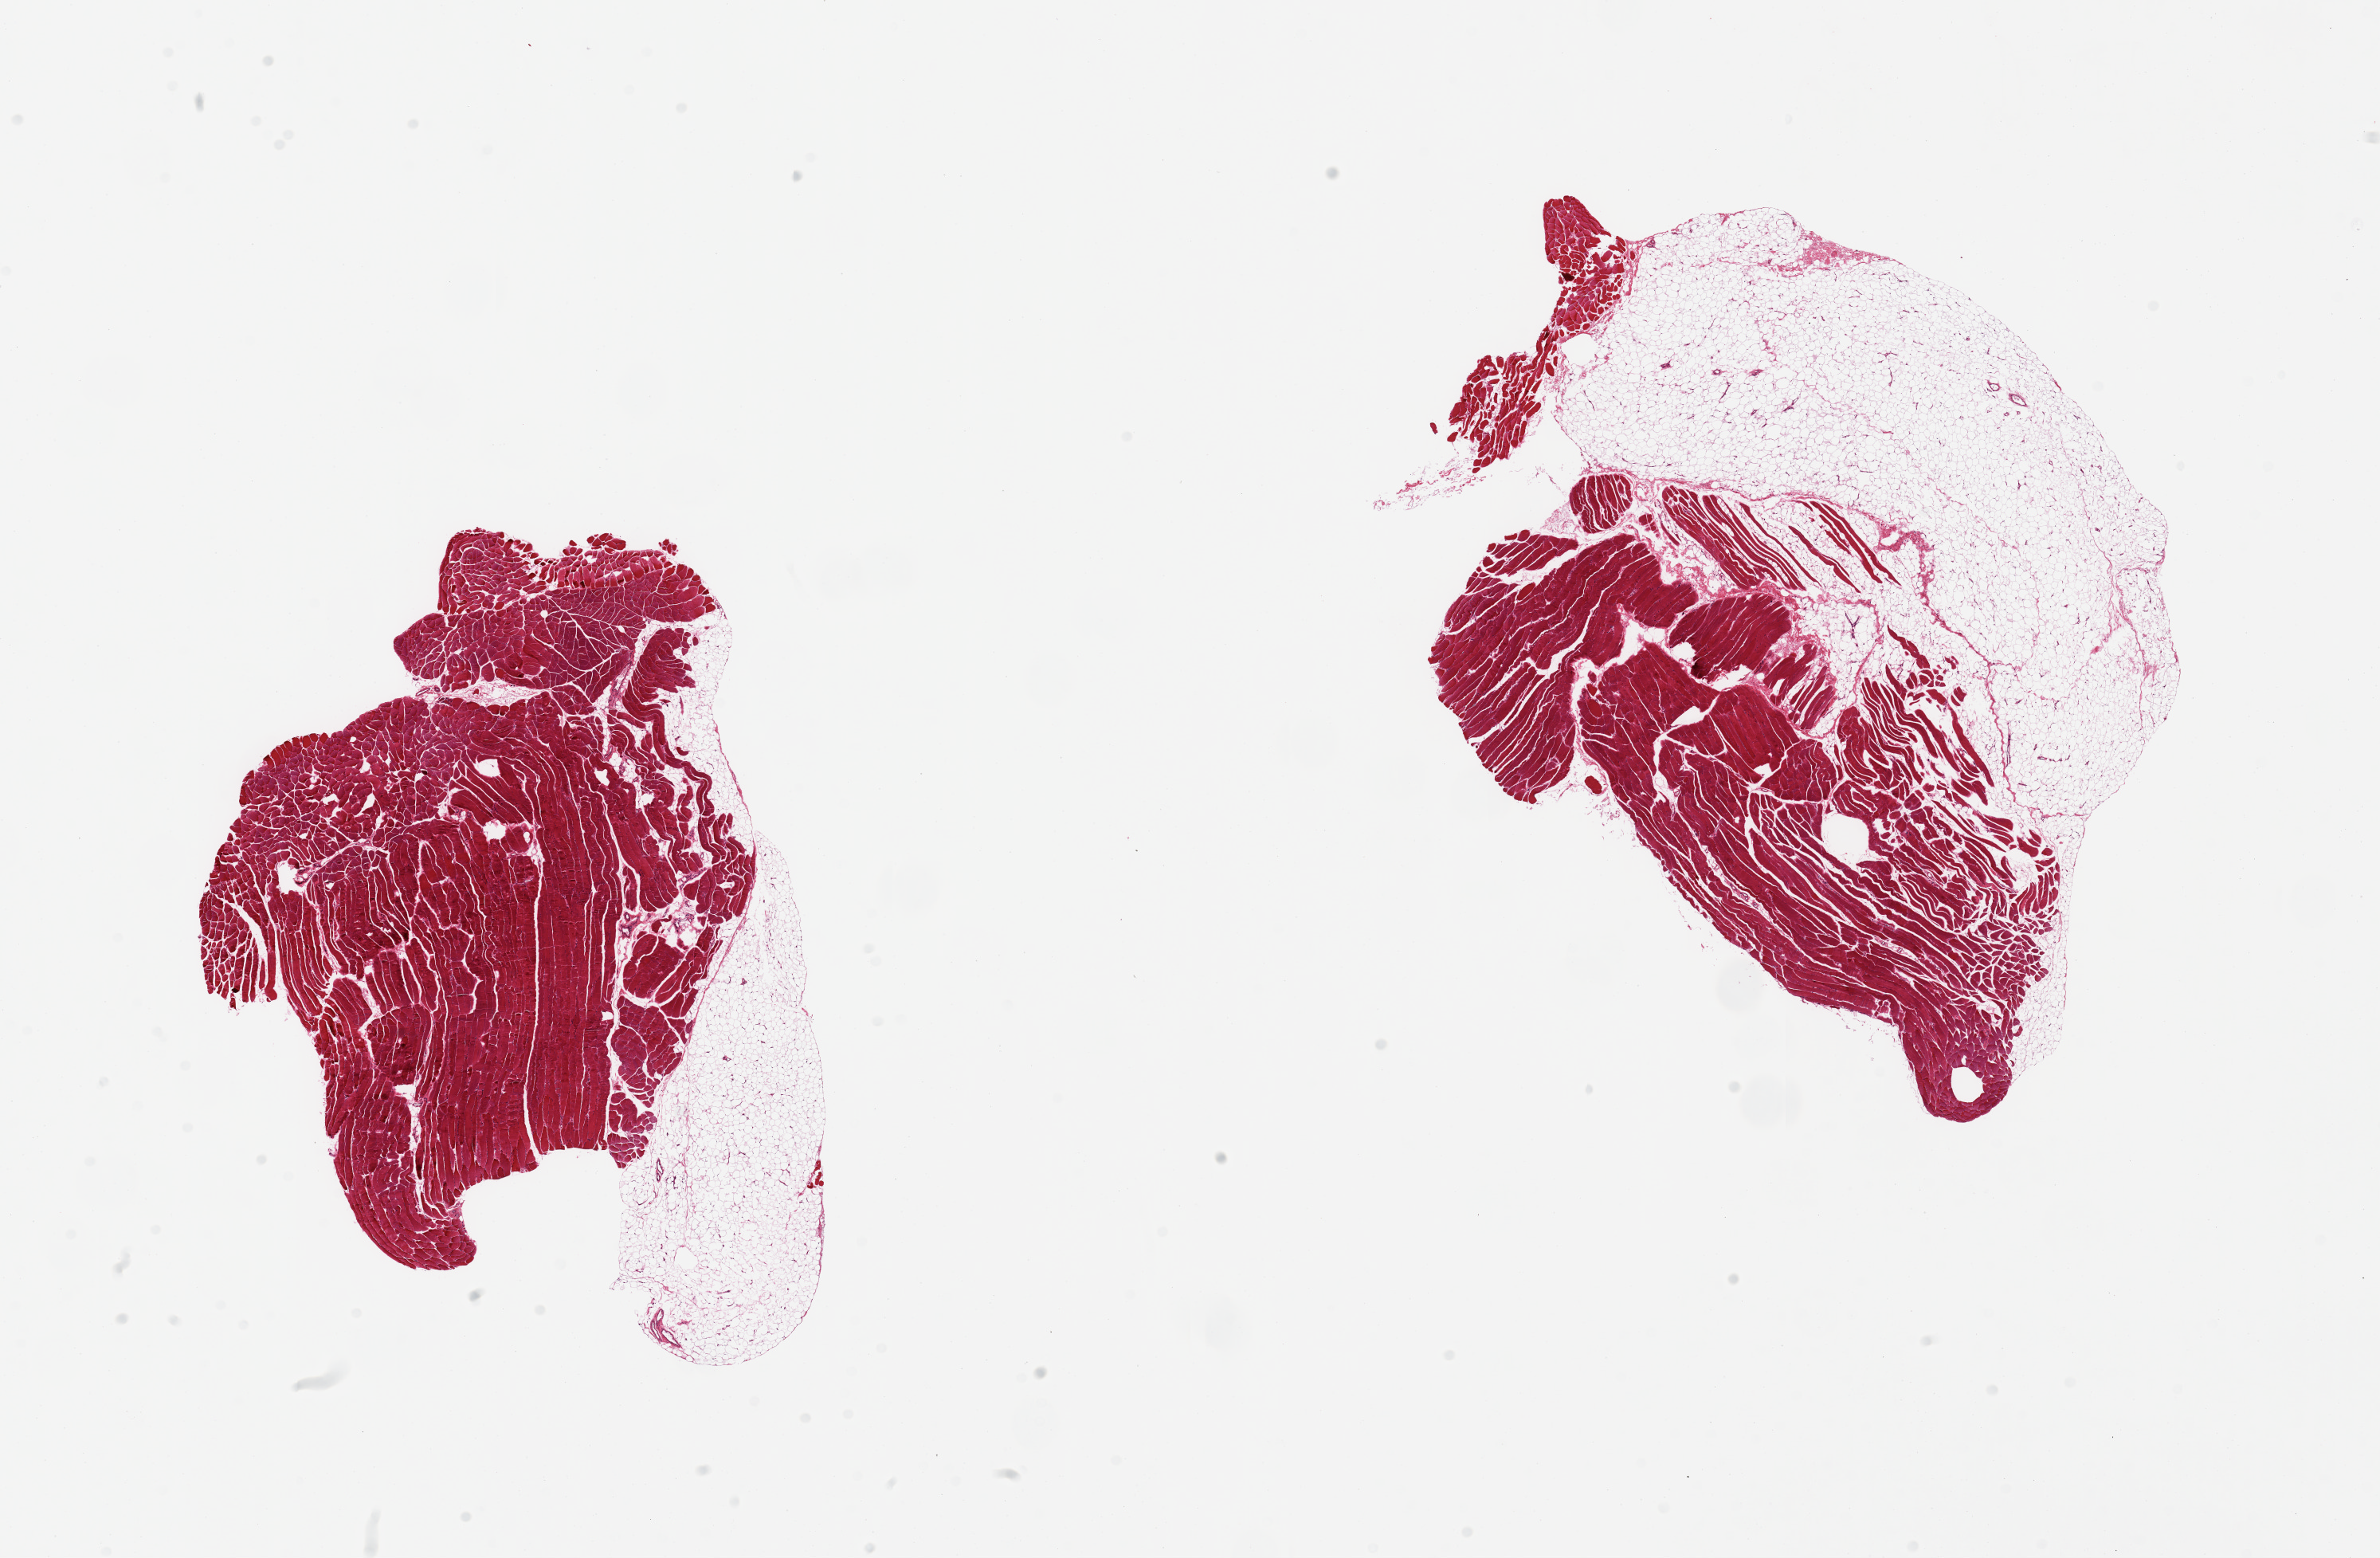
Whole-slide image, hematoxylin and eosin (H&E) stain, brightfield, whole scanned area (about 23.6 x 15.5 mm, acquisition: 20x scan) shown as a low-resolution overview, PAXgene-fixed paraffin-embedded (PFPE) section, section of skeletal muscle (target tissue), donor tissue sample. Donor sex: female.
* pathologist's review note for this sample: 2 pieces, both include attached fat (20 and 50%)